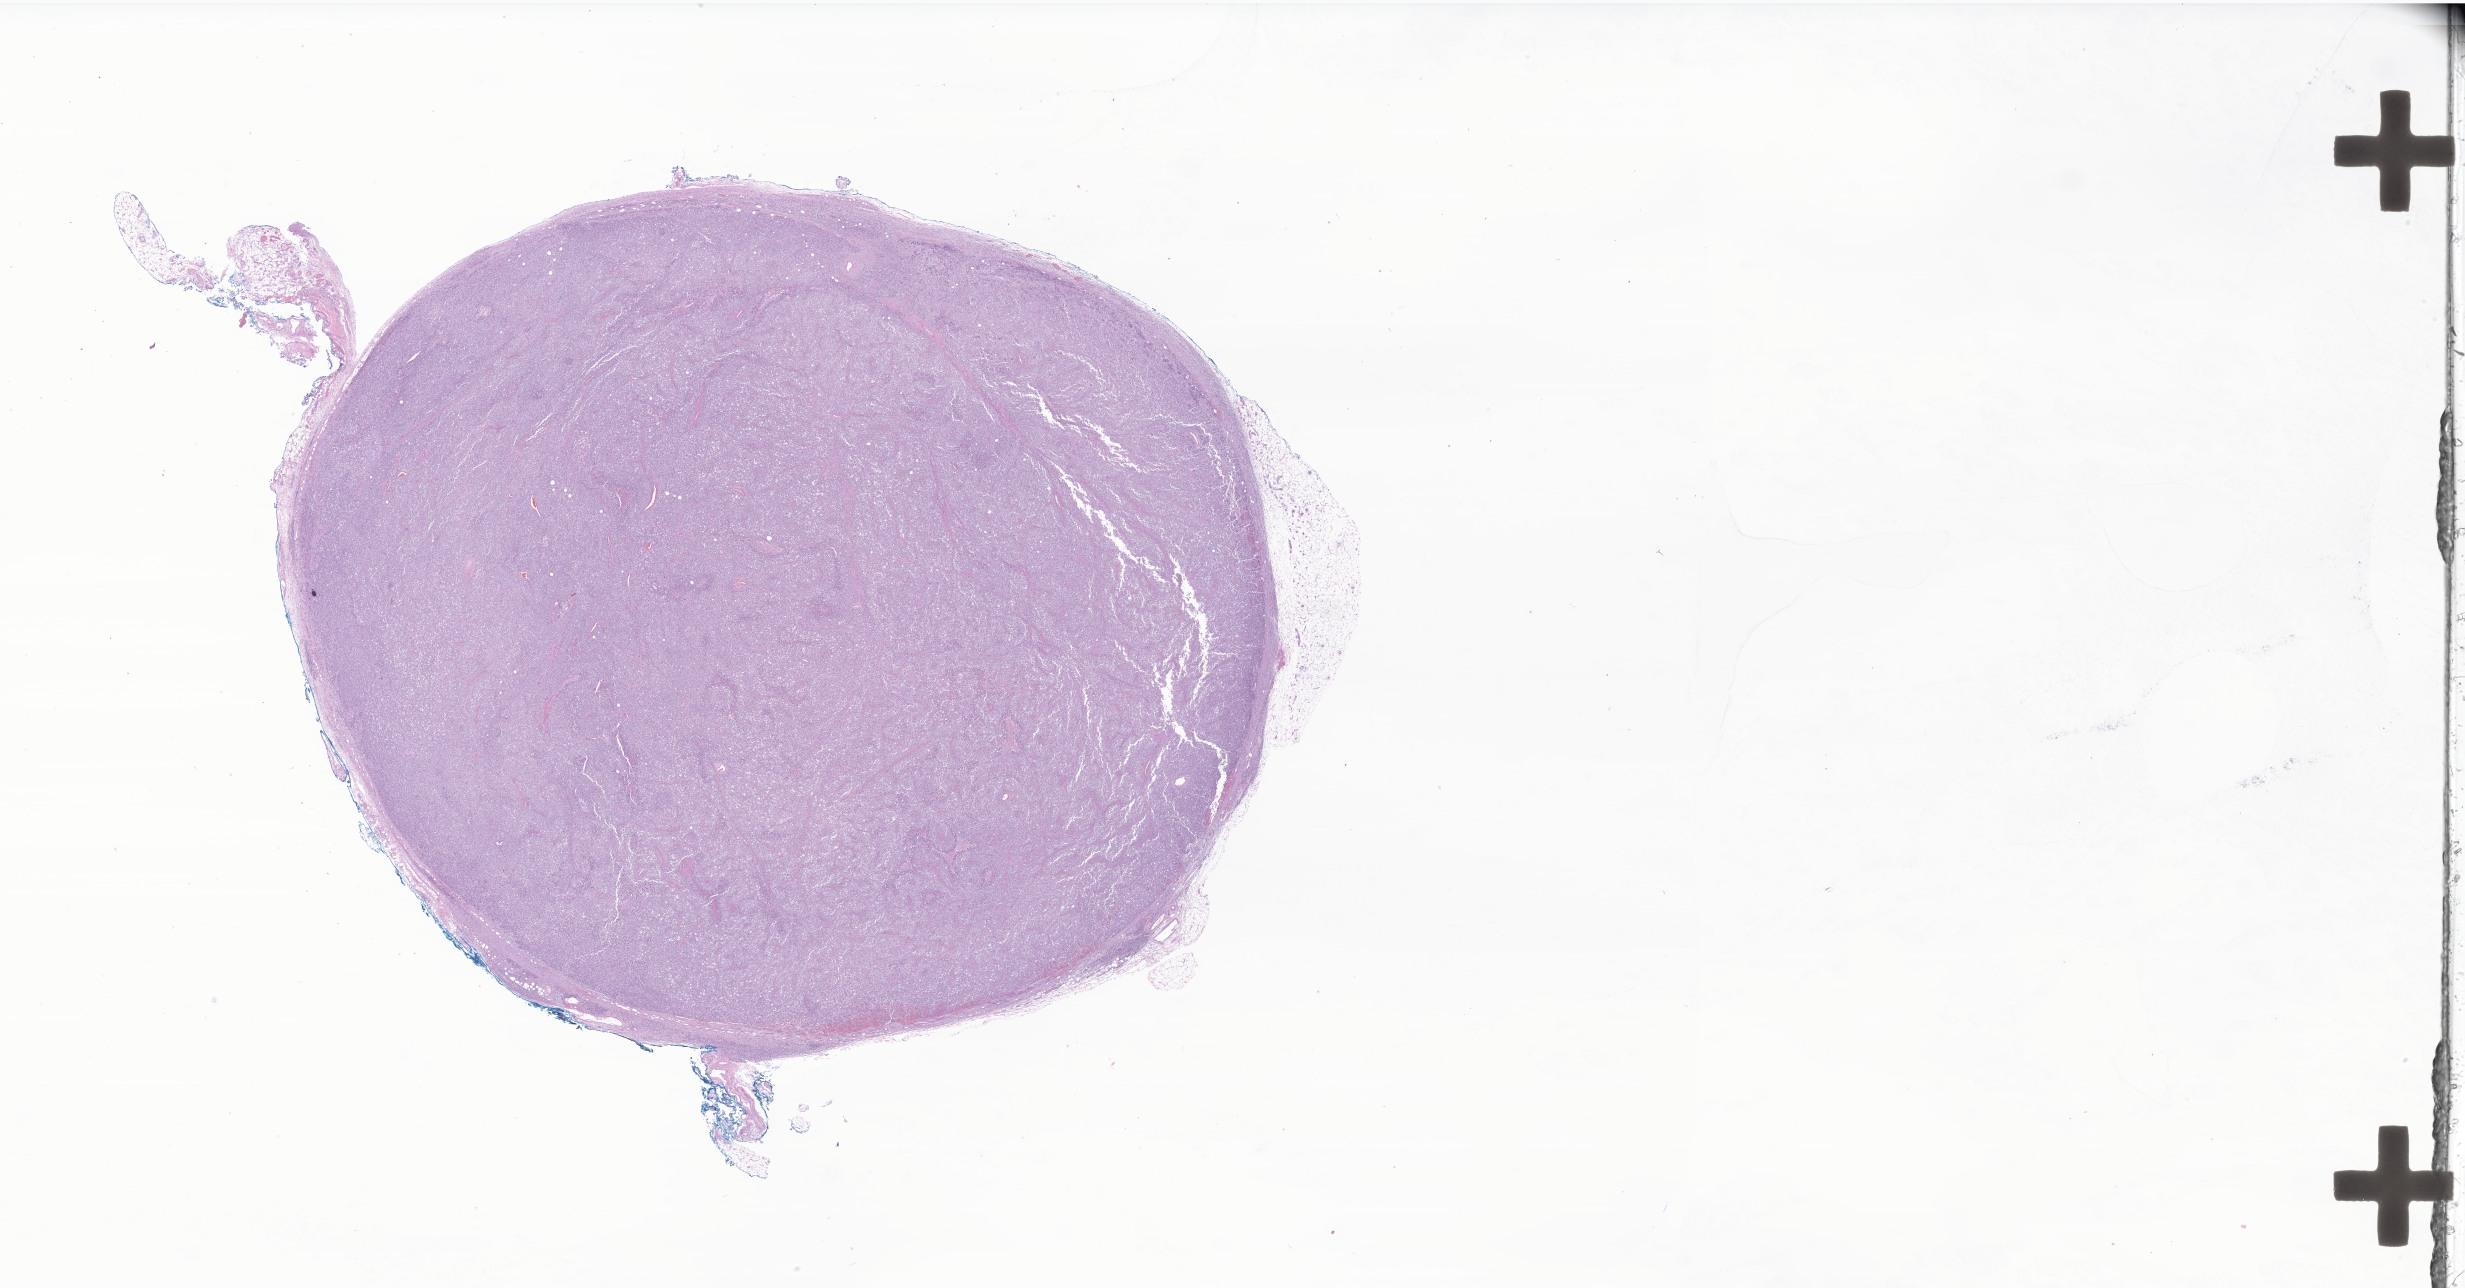
Haematoxylin and eosin whole-slide image of tumor tissue from the pelvis, shown as a low-resolution overview of the whole scanned area (about 41.6 x 21.7 mm); FFPE section. Male patient, age 221 months (18 years 5 months).
Recorded diagnosis: Rhabdomyosarcoma, NOS.